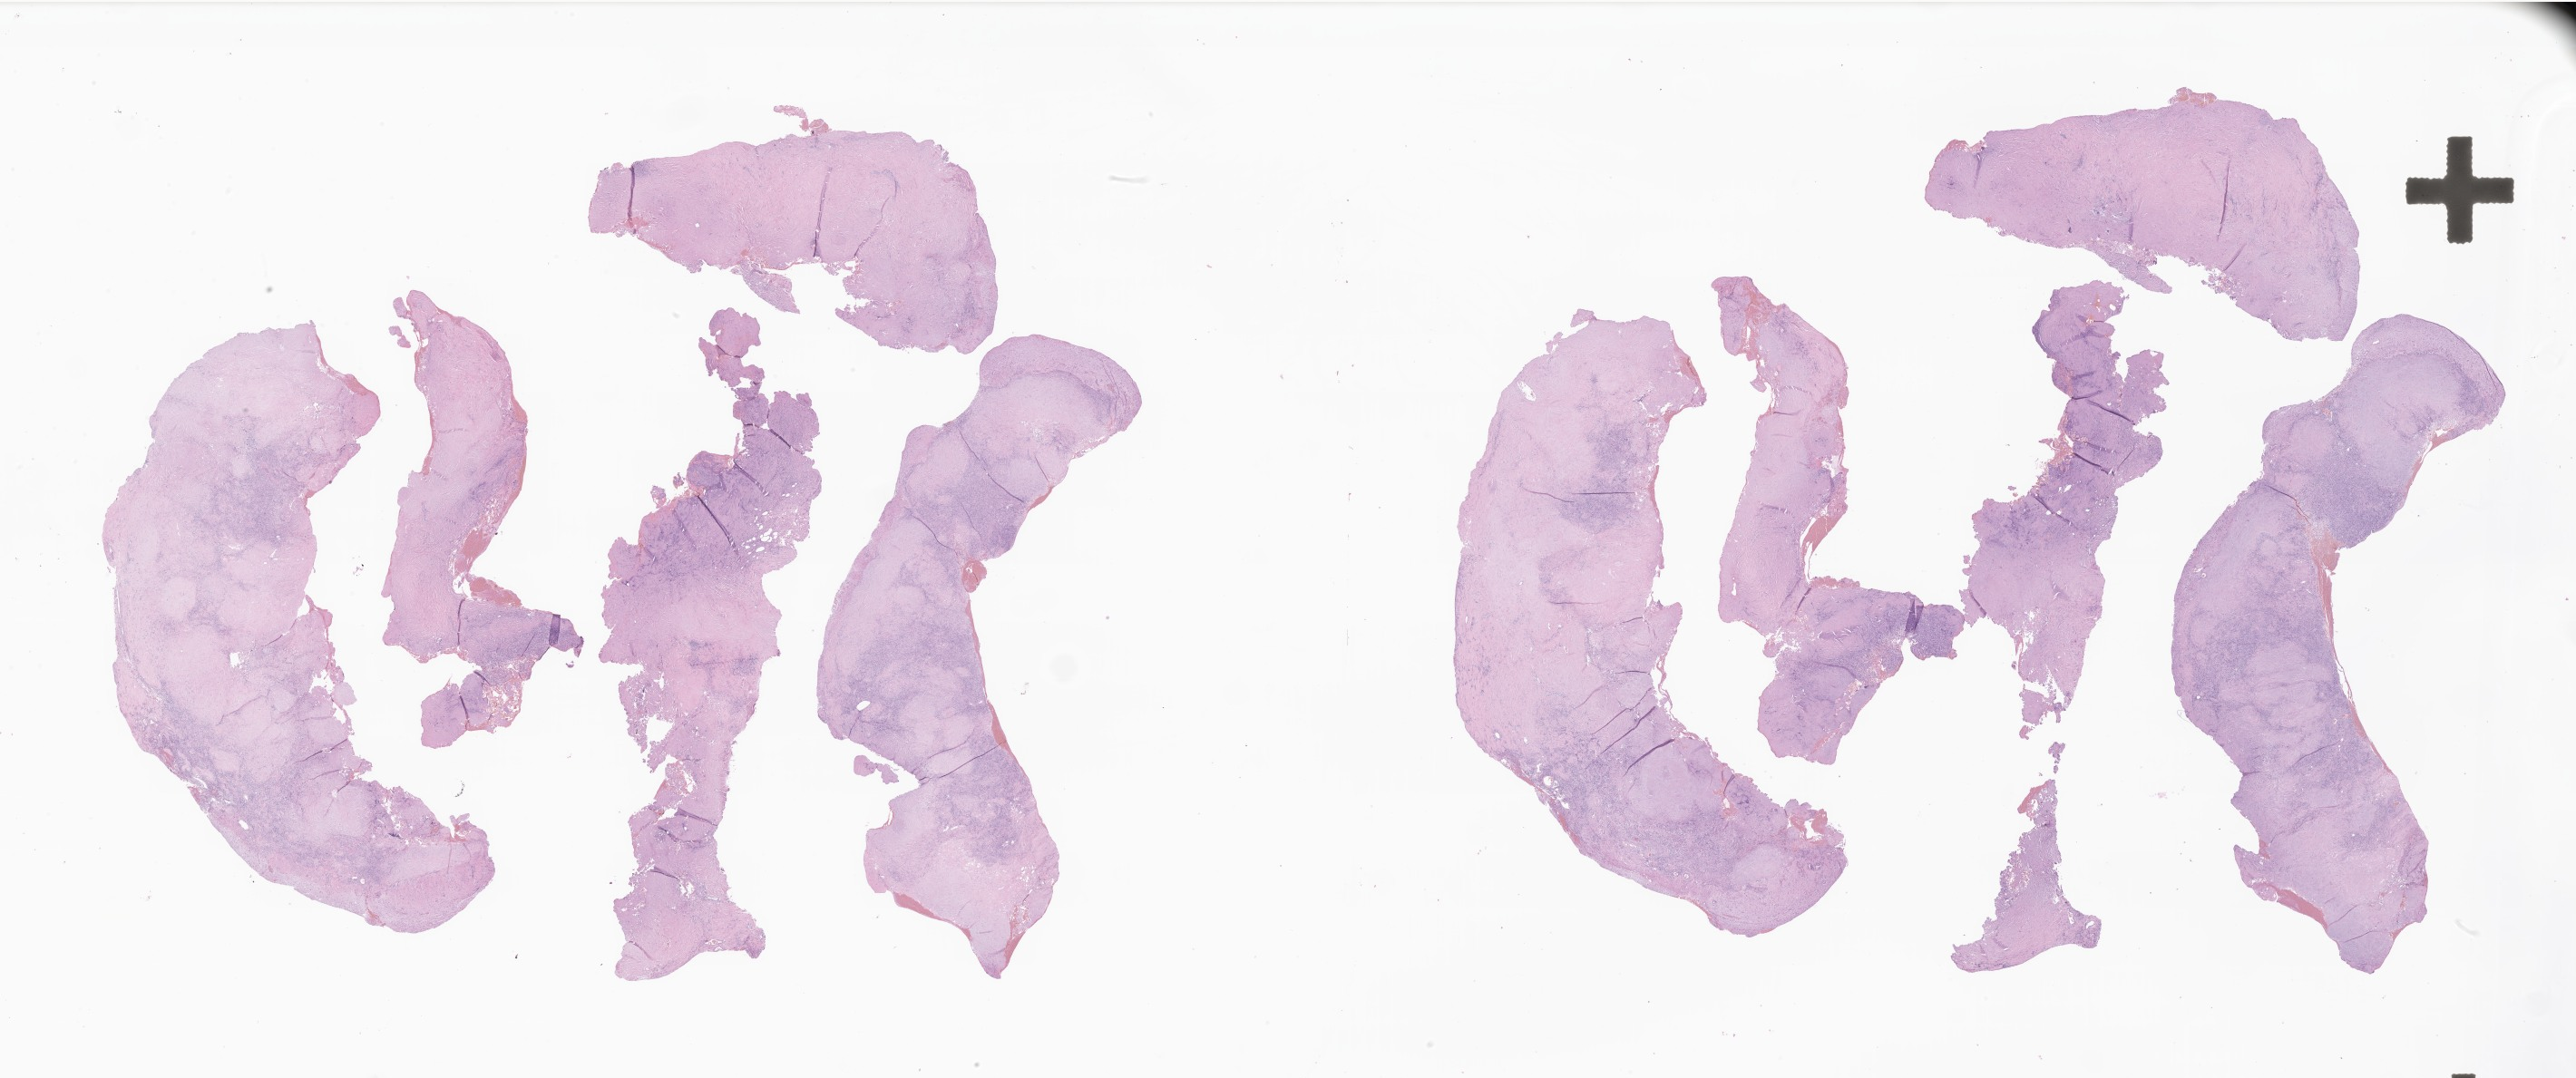
Digitized hematoxylin and eosin (H&E)-stained section of tumor tissue from the meninges, shown as a low-resolution overview of the whole scanned area (about 47.9 x 20.1 mm). Formalin-fixed paraffin-embedded section. Patient male; age 69 months (5 years 9 months).
Diagnosis: Meningioma, NOS.